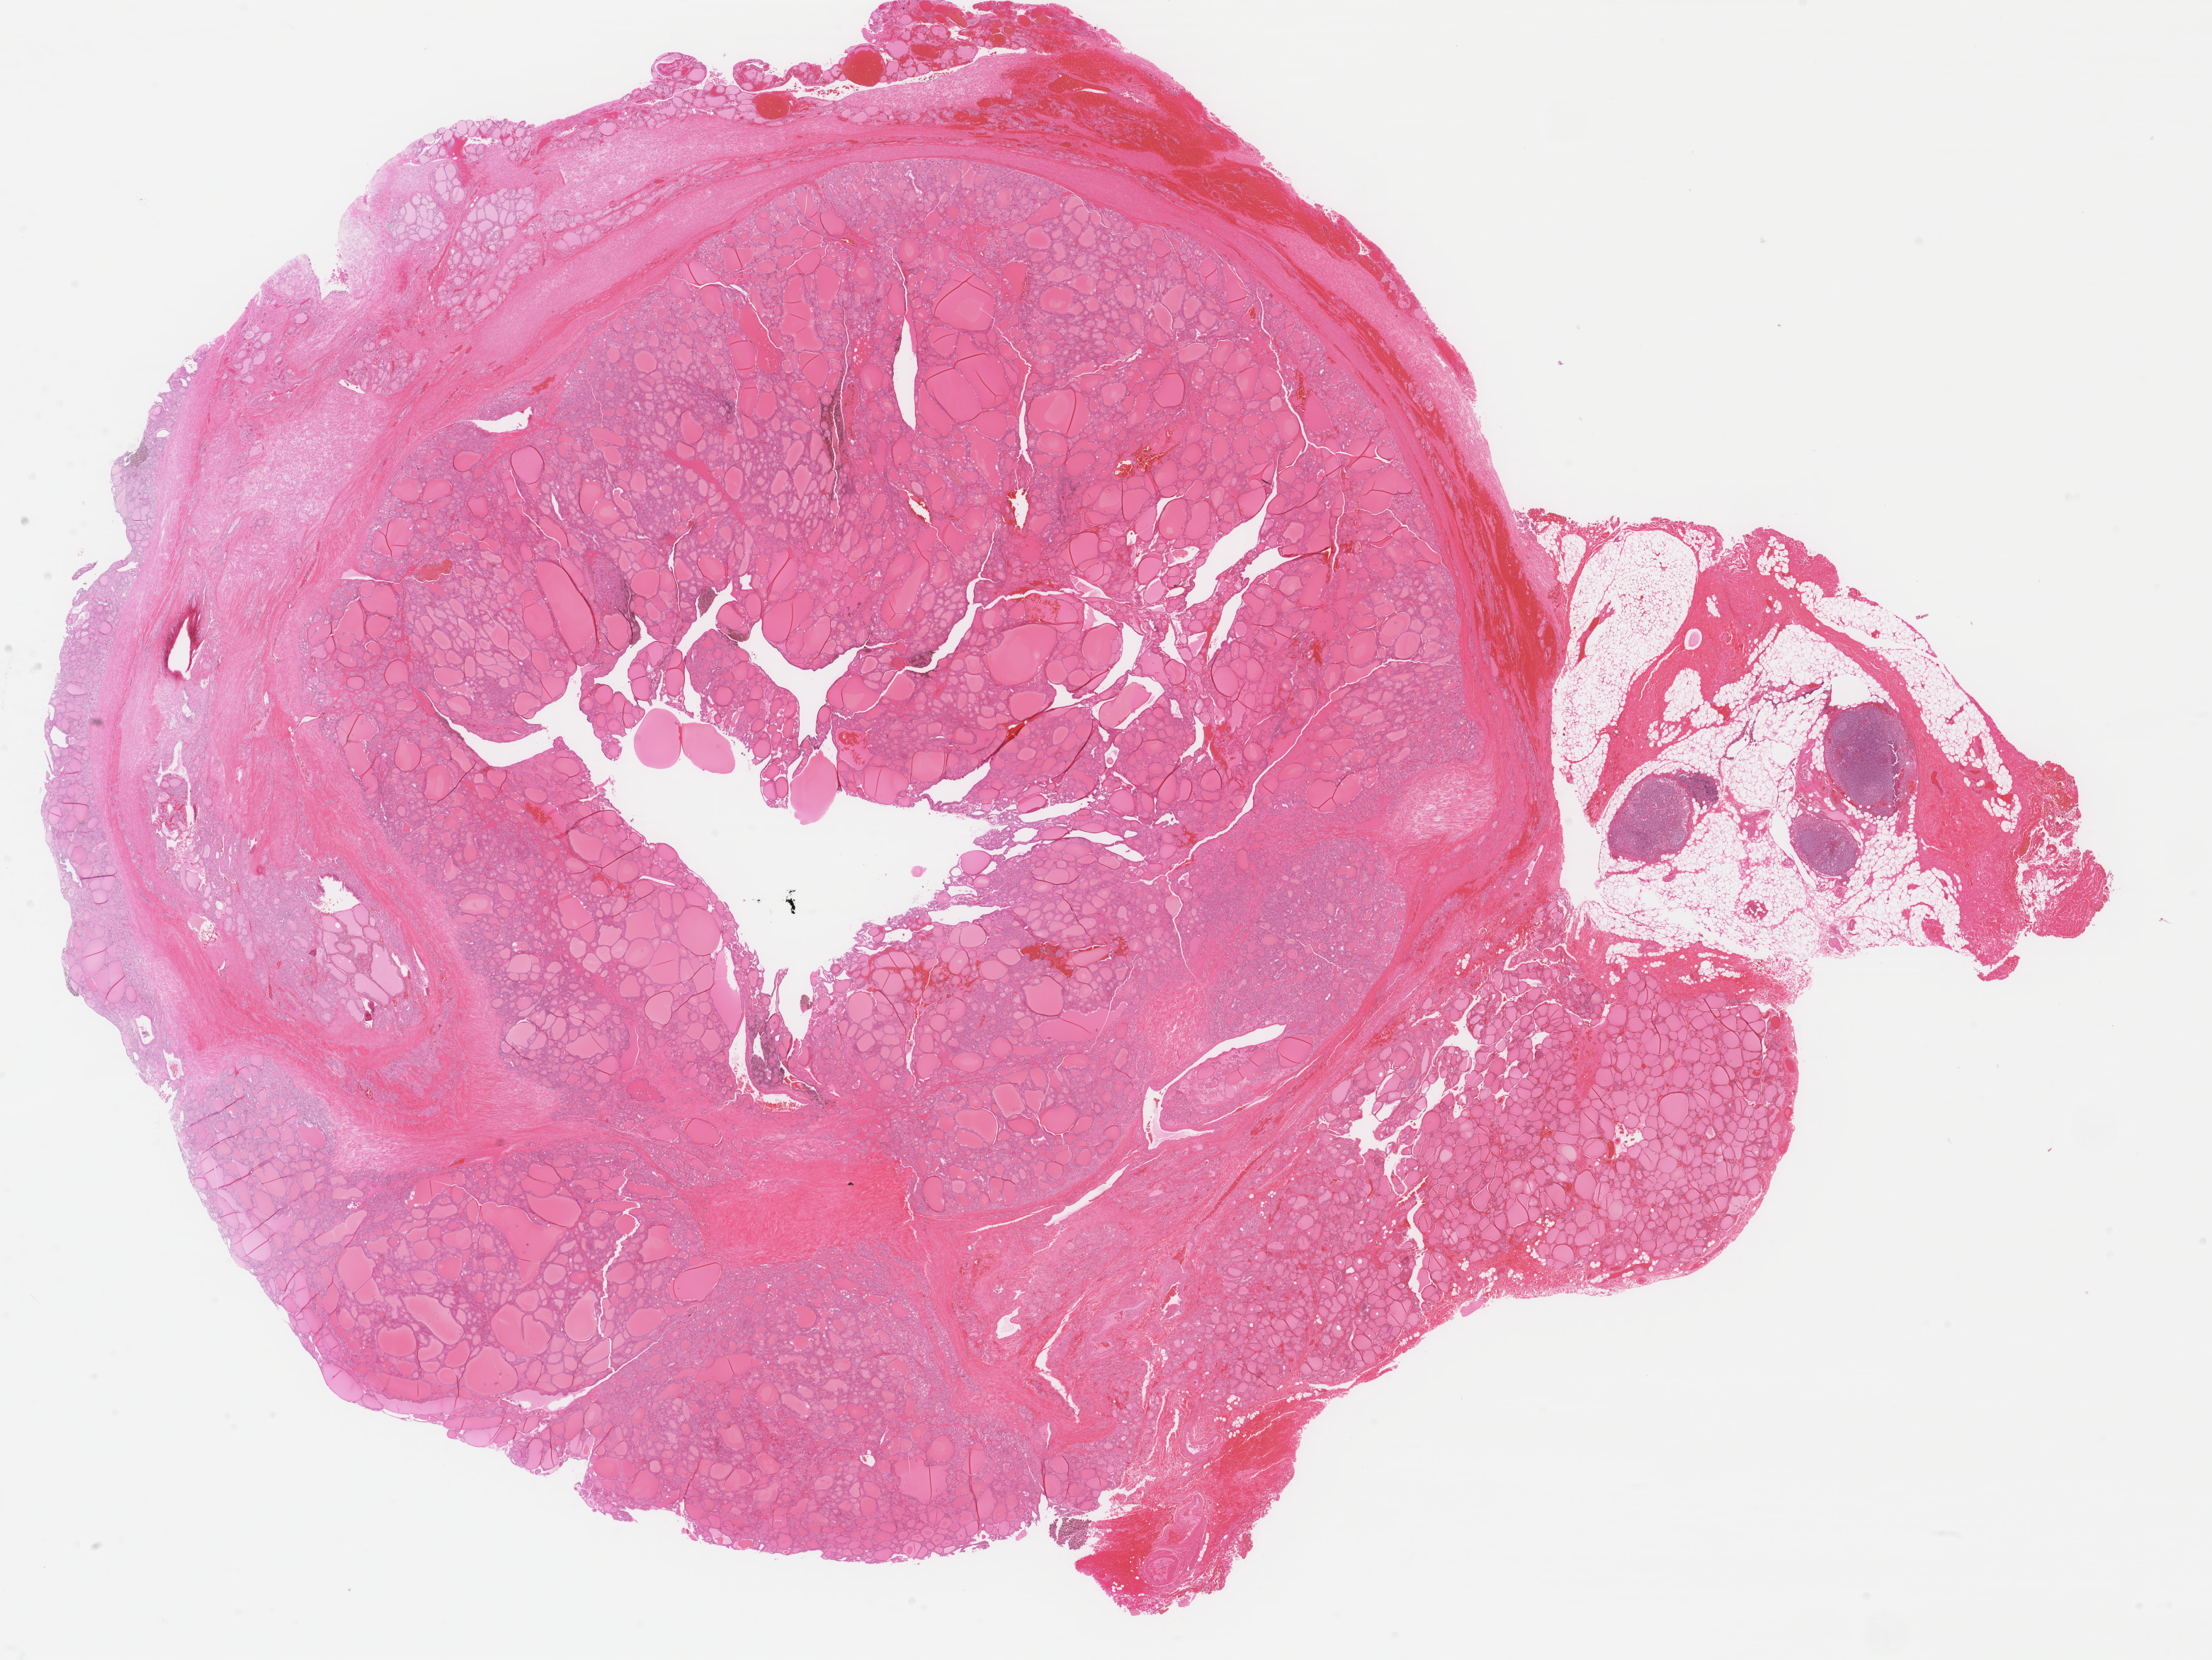
Whole-slide histology image, H&E — whole scanned area (about 24.8 x 18.6 mm, acquisition: 40x scan) shown as a low-resolution overview. FFPE section. Sample: primary tumour, thyroid. Female, age 37 years at initial diagnosis.
Histologic diagnosis: Papillary adenocarcinoma, NOS.